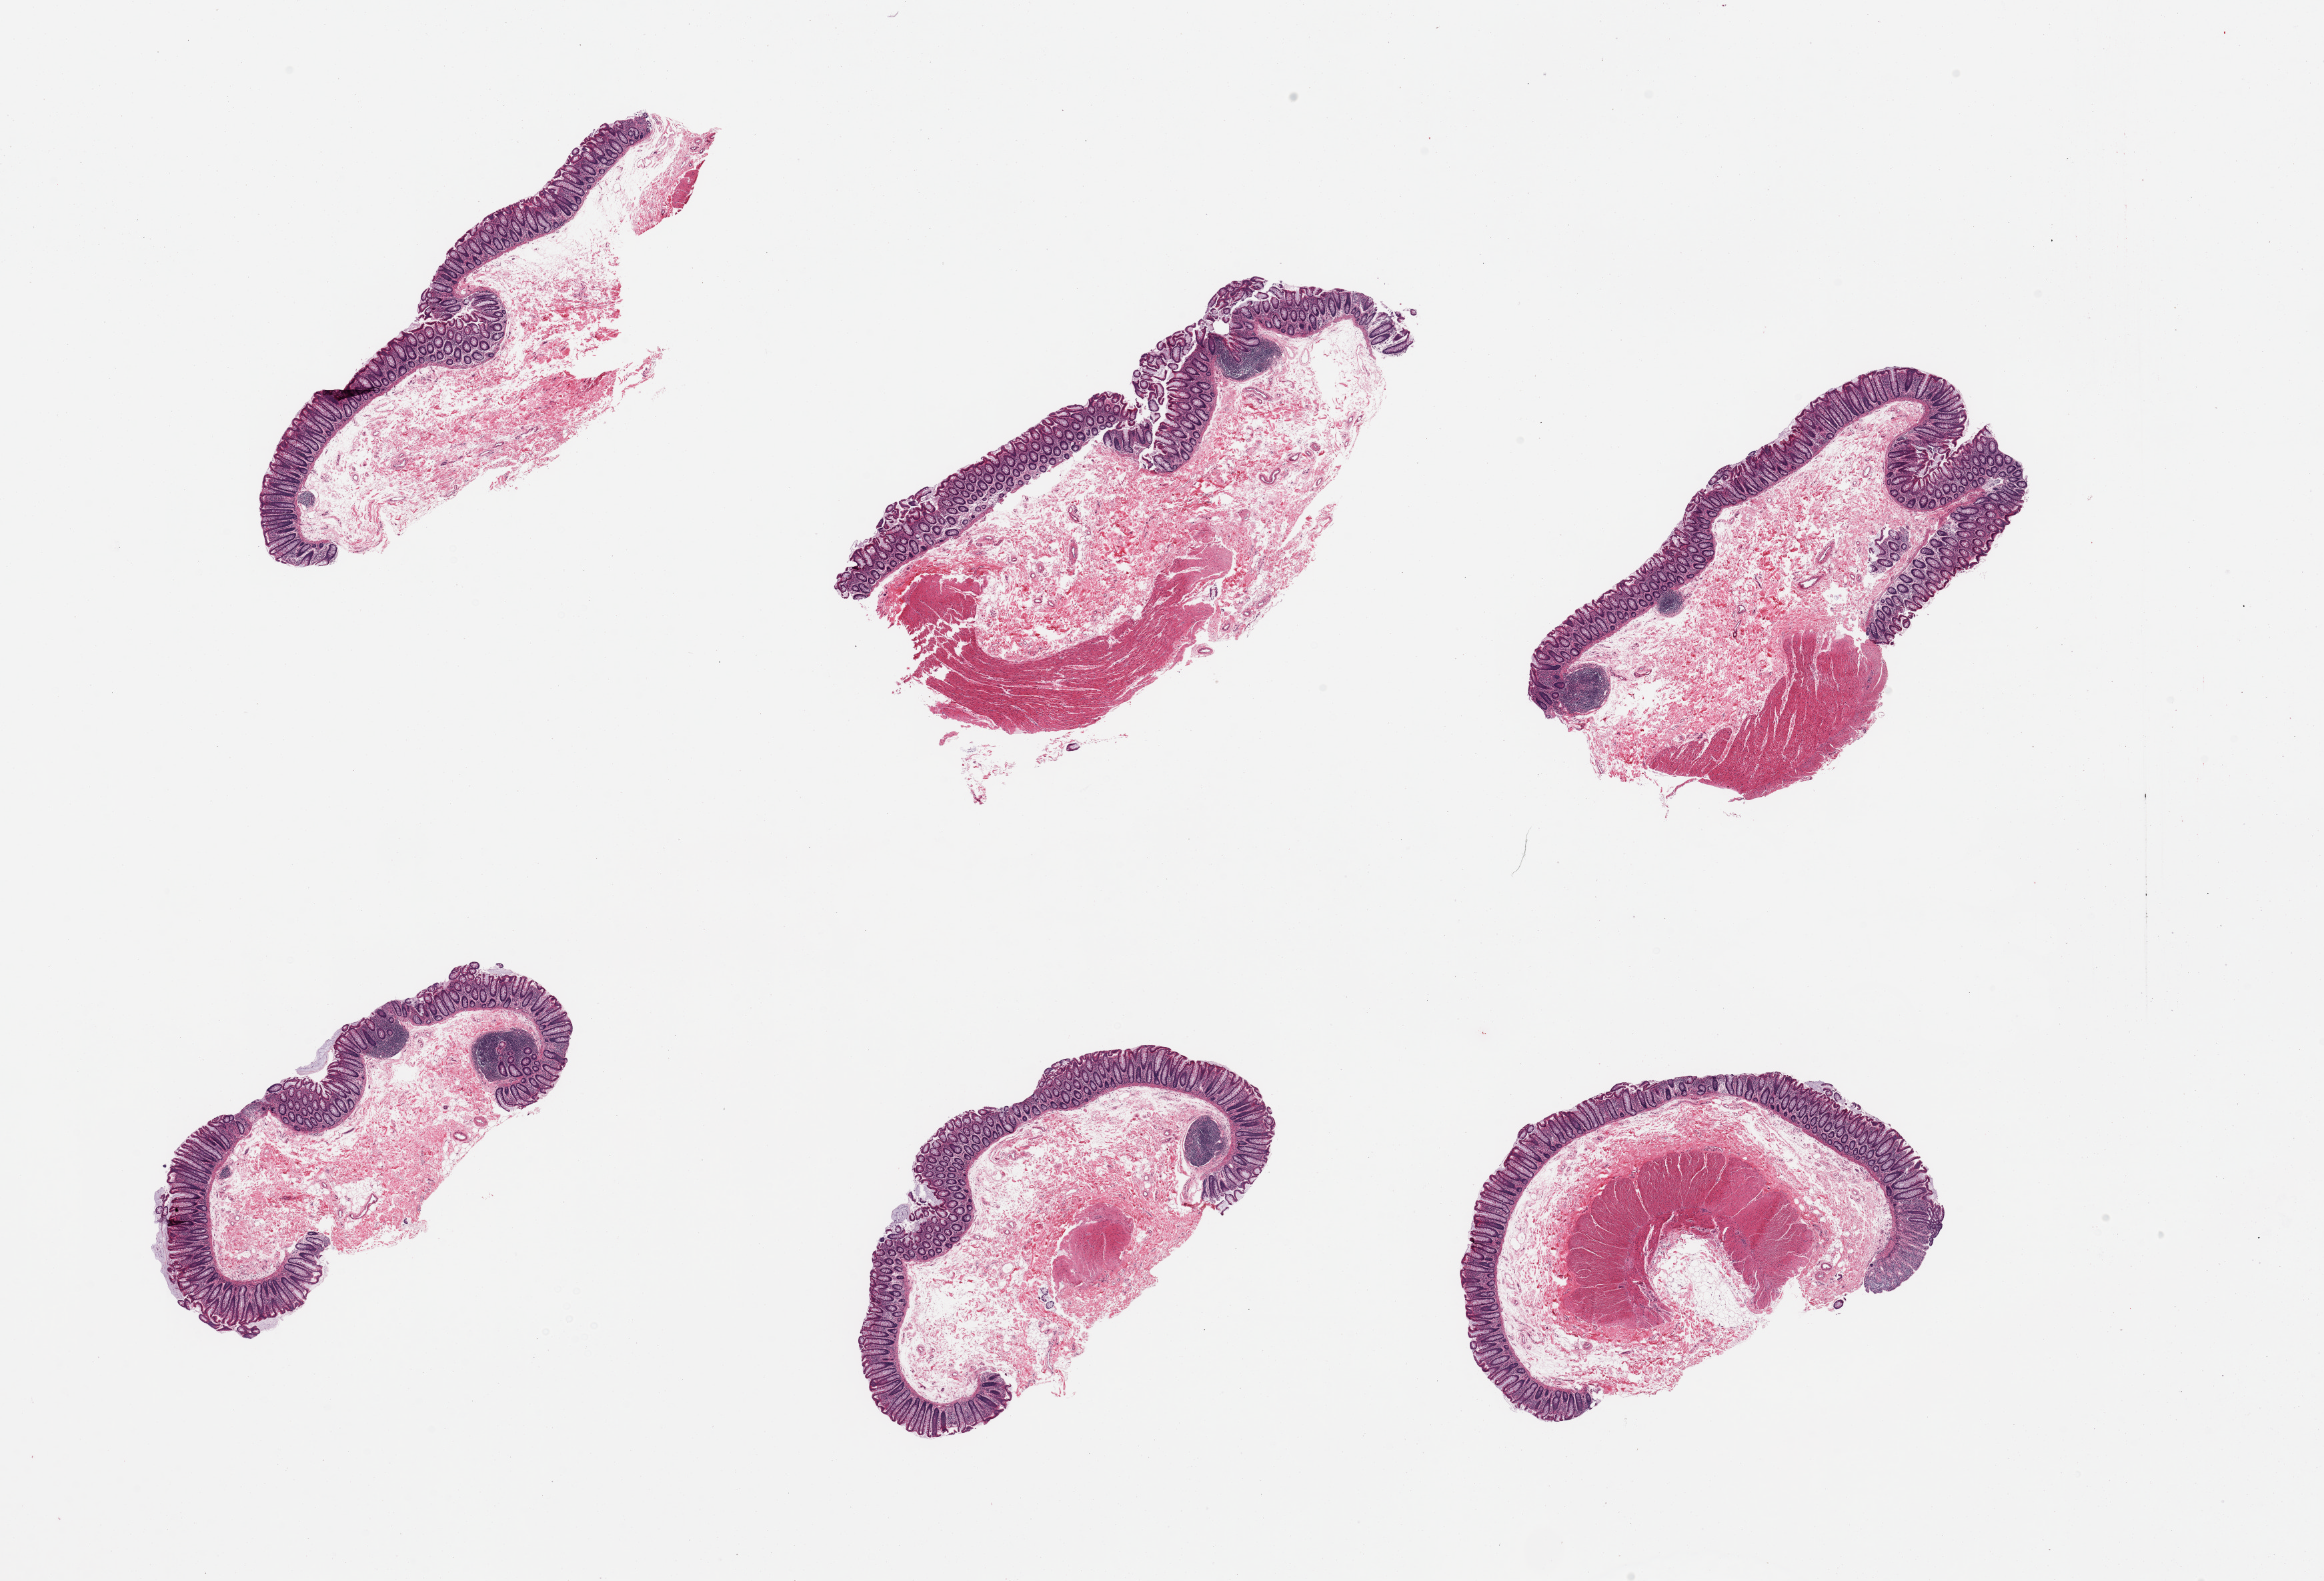
Haematoxylin and eosin whole-slide image — shown as a low-resolution overview of the whole scanned area (about 27.6 x 18.8 mm, slide scanned at 20x). Donor sex: male.
Specimen: PAXgene-fixed paraffin-embedded (PFPE) section; target tissue: transverse colon; donor tissue sample.